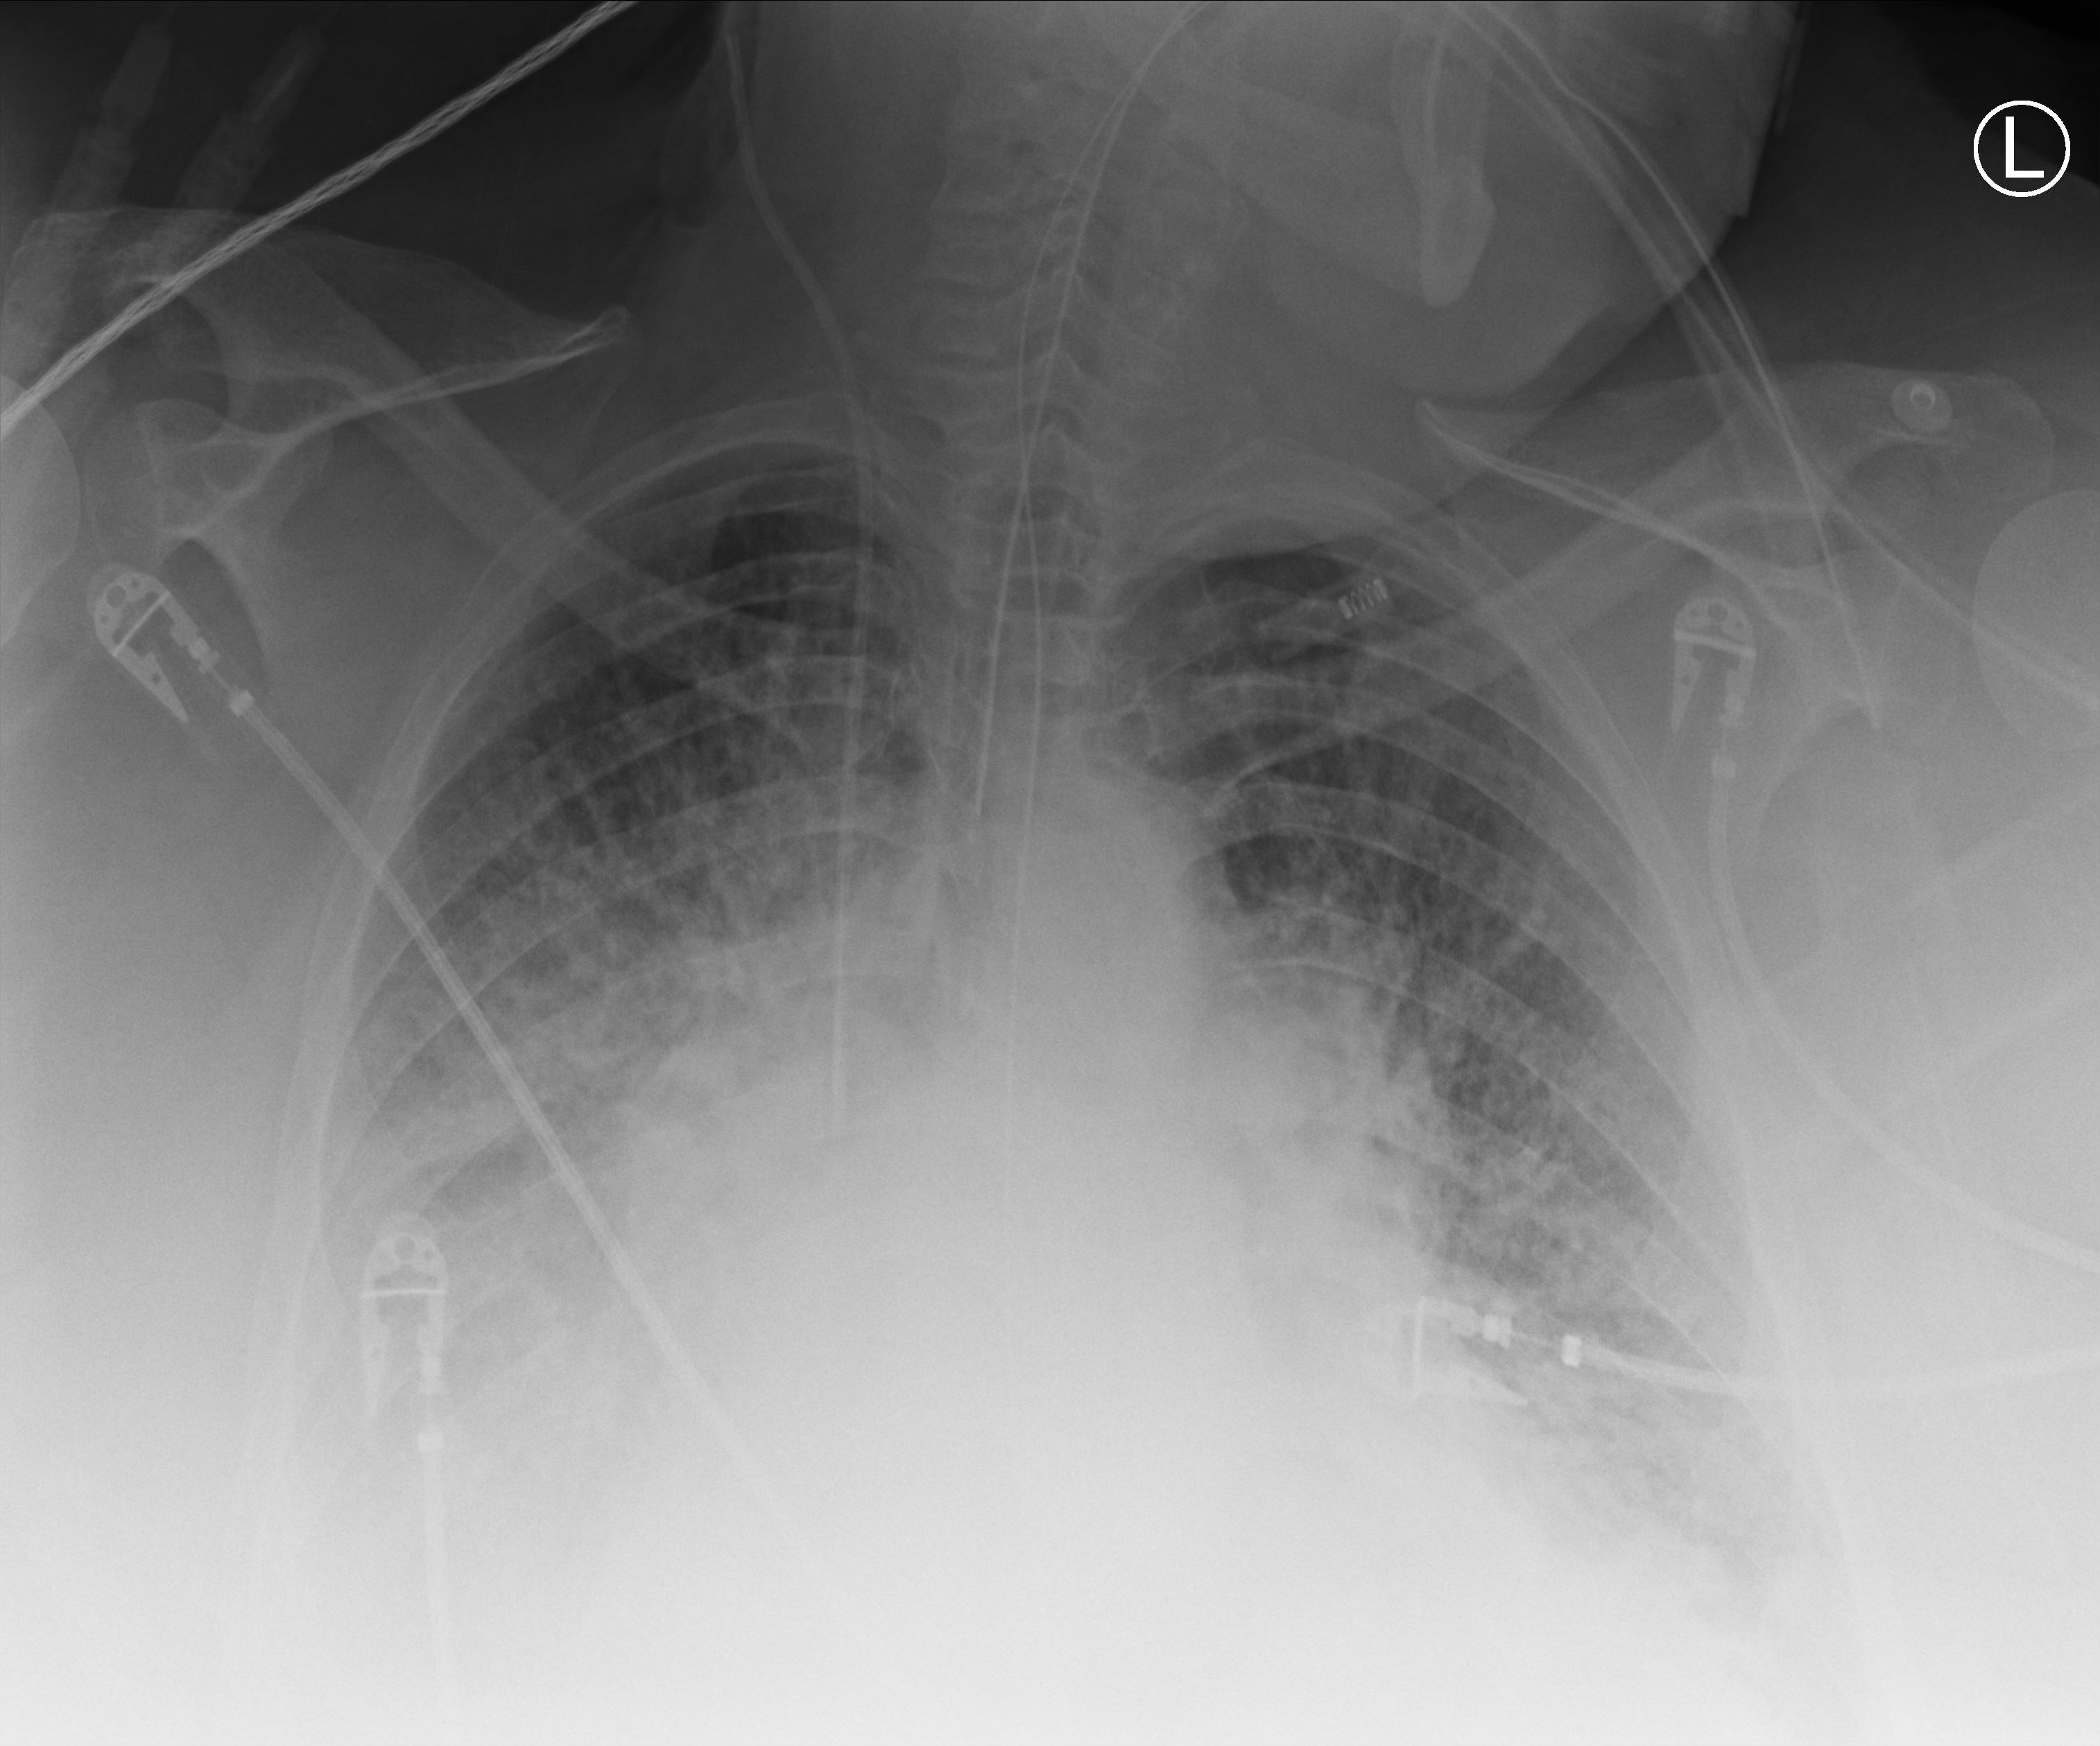
Chest X-ray (portable), anteroposterior (AP) projection. Patient hospitalised with COVID-19; female, aged 60–74 years.
Admission-level facts for this patient (not findings on this image; timing relative to this image not recorded):
- other chronic lung disease (admission record): no